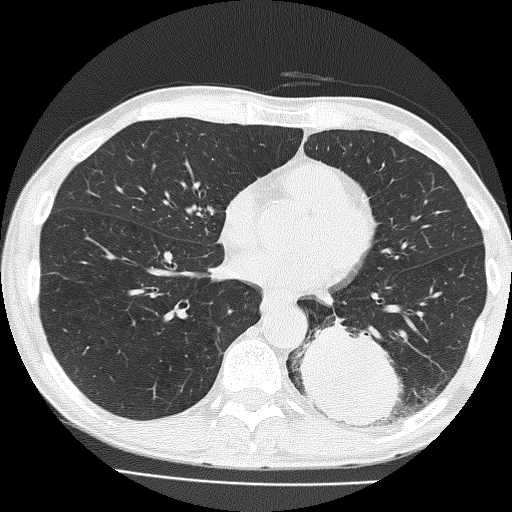
Low-dose screening chest CT, axial slice; baseline screening round; lung window (W 1500 / L -600 HU); slice 92 of 160 in the series. Male participant, aged 58 years at enrolment.
Expert-annotated lung lesion, bounding box <299,308,422,434> (left, top, right, bottom; pixels). The screening reader recorded 2 non-calcified nodules or masses ≥4 mm on this exam (left lower lobe, left upper lobe); which of them this box marks is not recorded. Official screen result: positive, change unspecified: nodule(s) >= 4 mm or enlarging nodule(s), mass(es), or other non-specific abnormalities suspicious for lung cancer. Later outcome: lung cancer diagnosed 39 days after this screen — non-small cell carcinoma, left lower lobe, poorly differentiated (G3), stage IV (AJCC 6th edition), 74 mm at pathology.